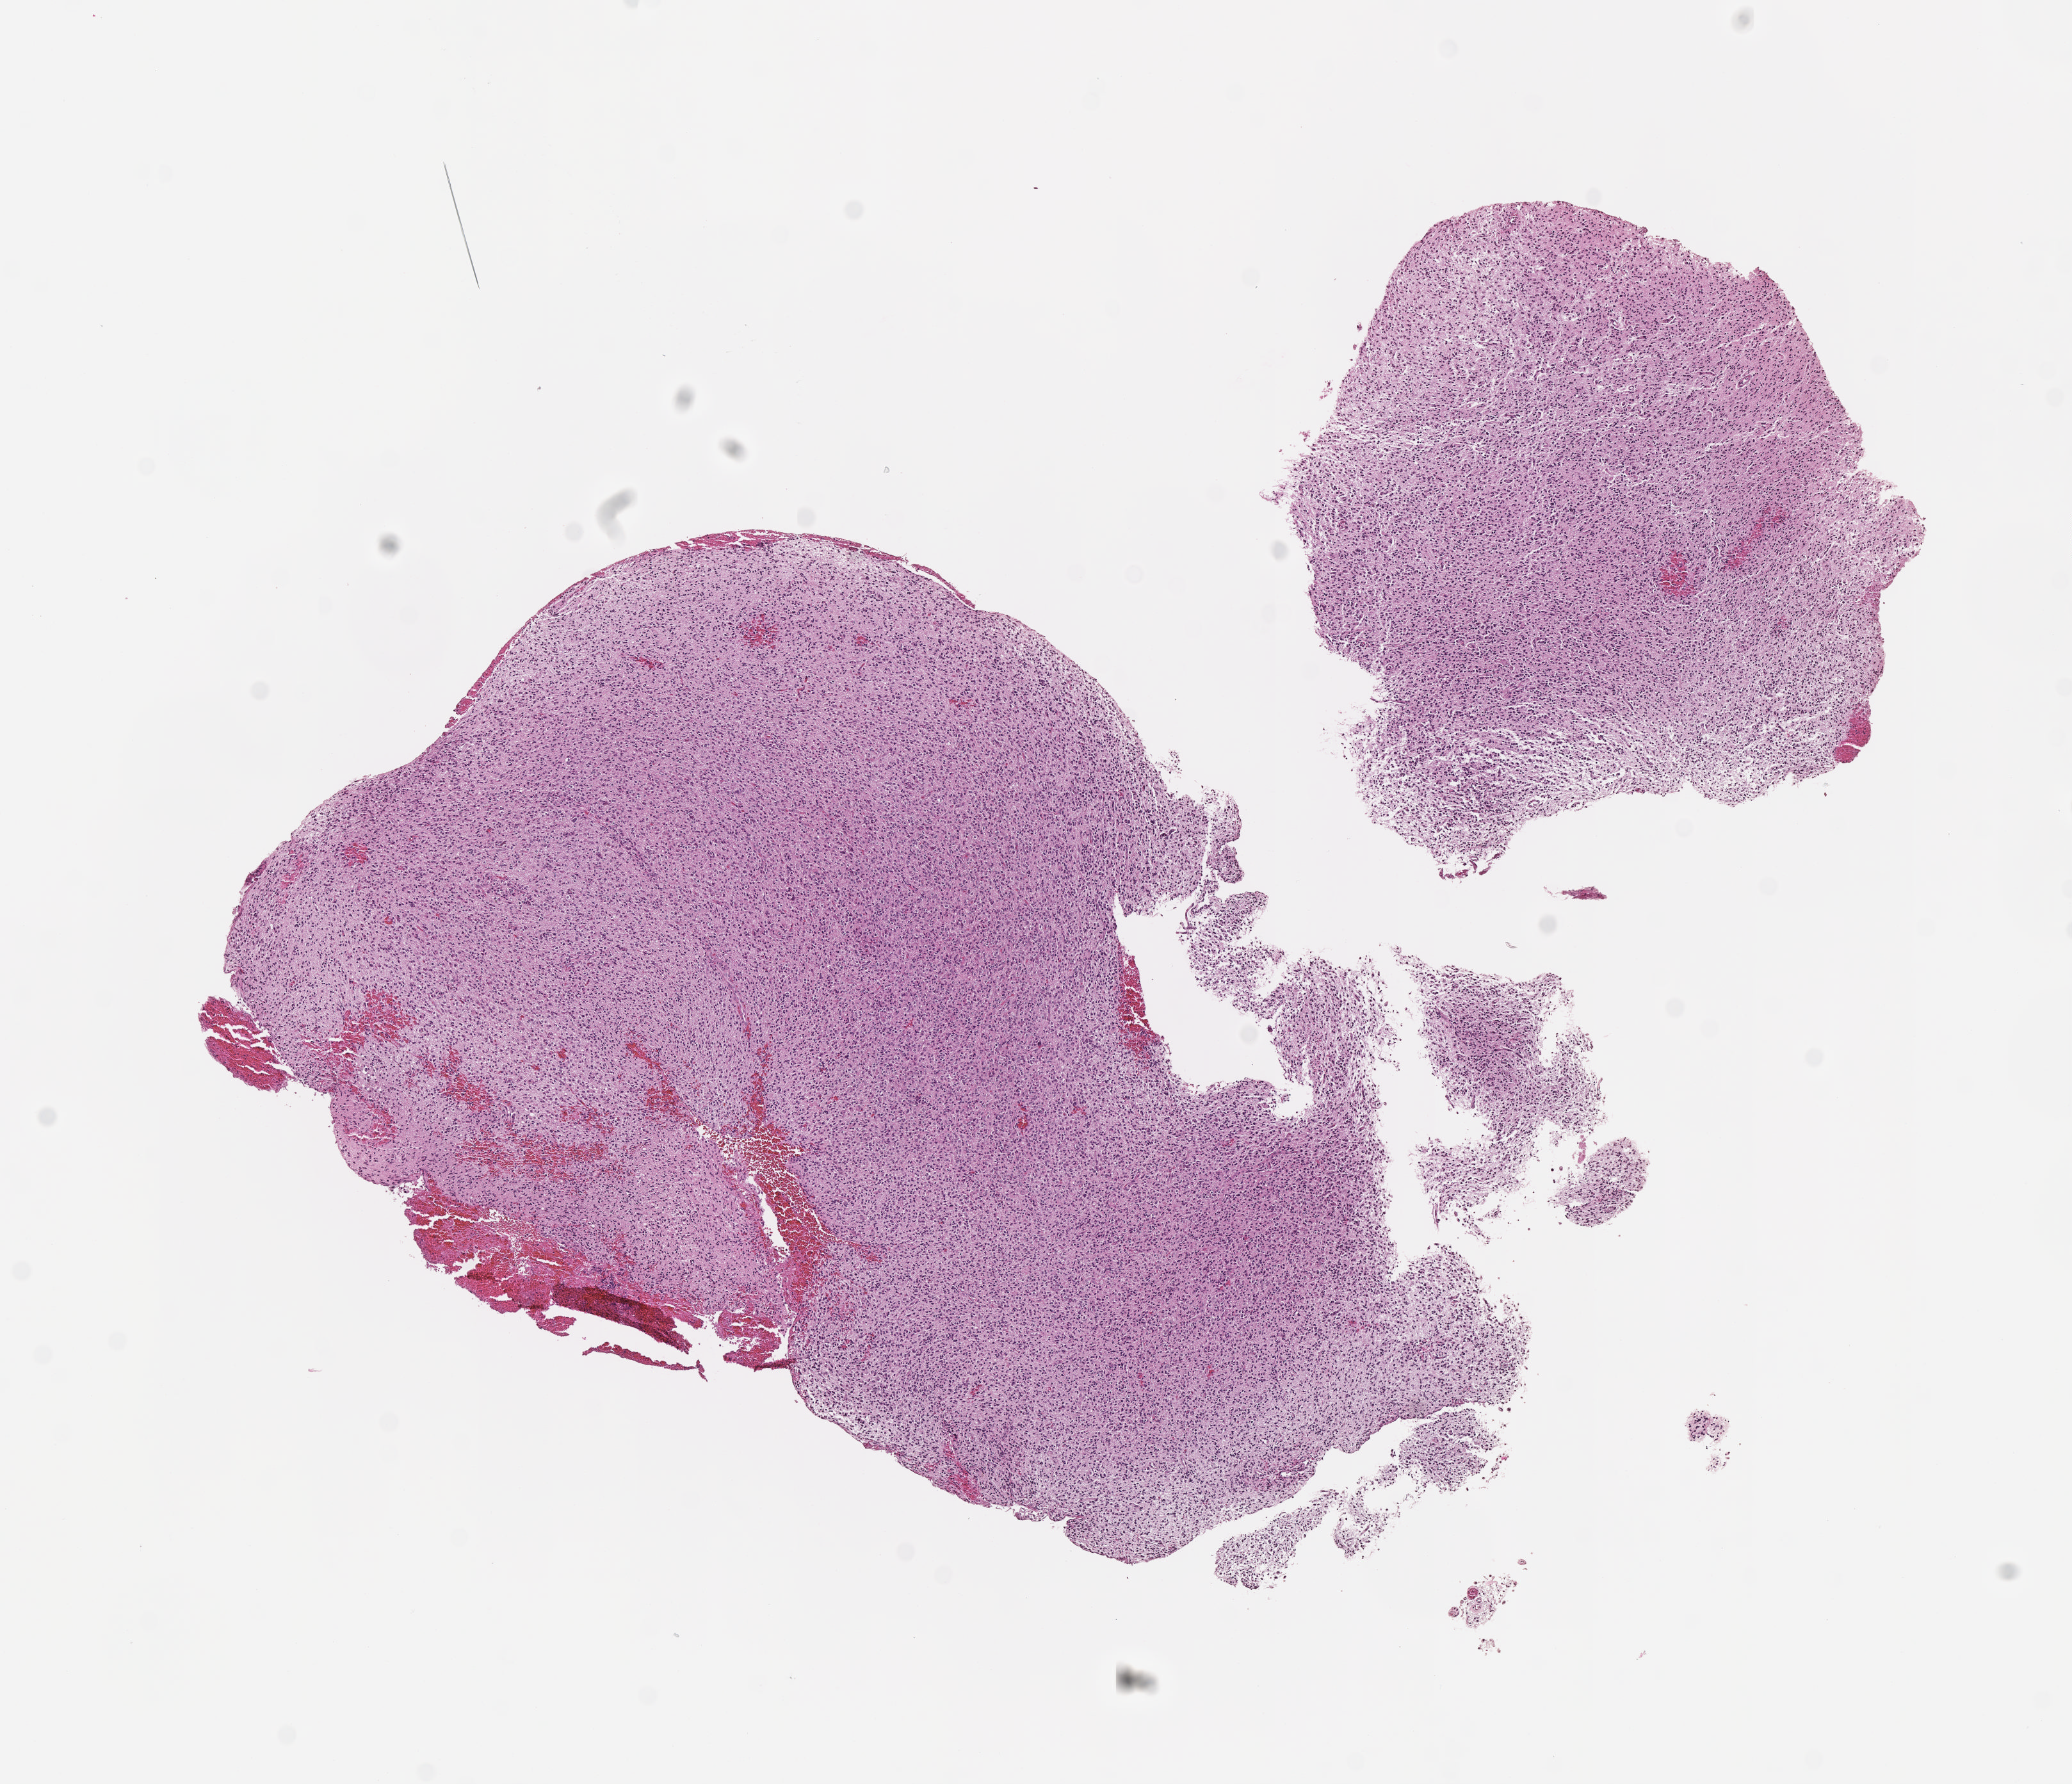
Whole-slide histology image, Hematoxylin and eosin (H&E) stained — shown as a low-resolution overview of the whole scanned area (about 6.5 x 5.6 mm, acquisition: 40x scan); formalin-fixed paraffin-embedded (FFPE) diagnostic section; brain, primary tumour sample. Male patient; age at initial diagnosis 52 years. Histologic grade: G3 (poorly differentiated).
Histologic diagnosis: Mixed glioma (cerebrum). Laterality: right.